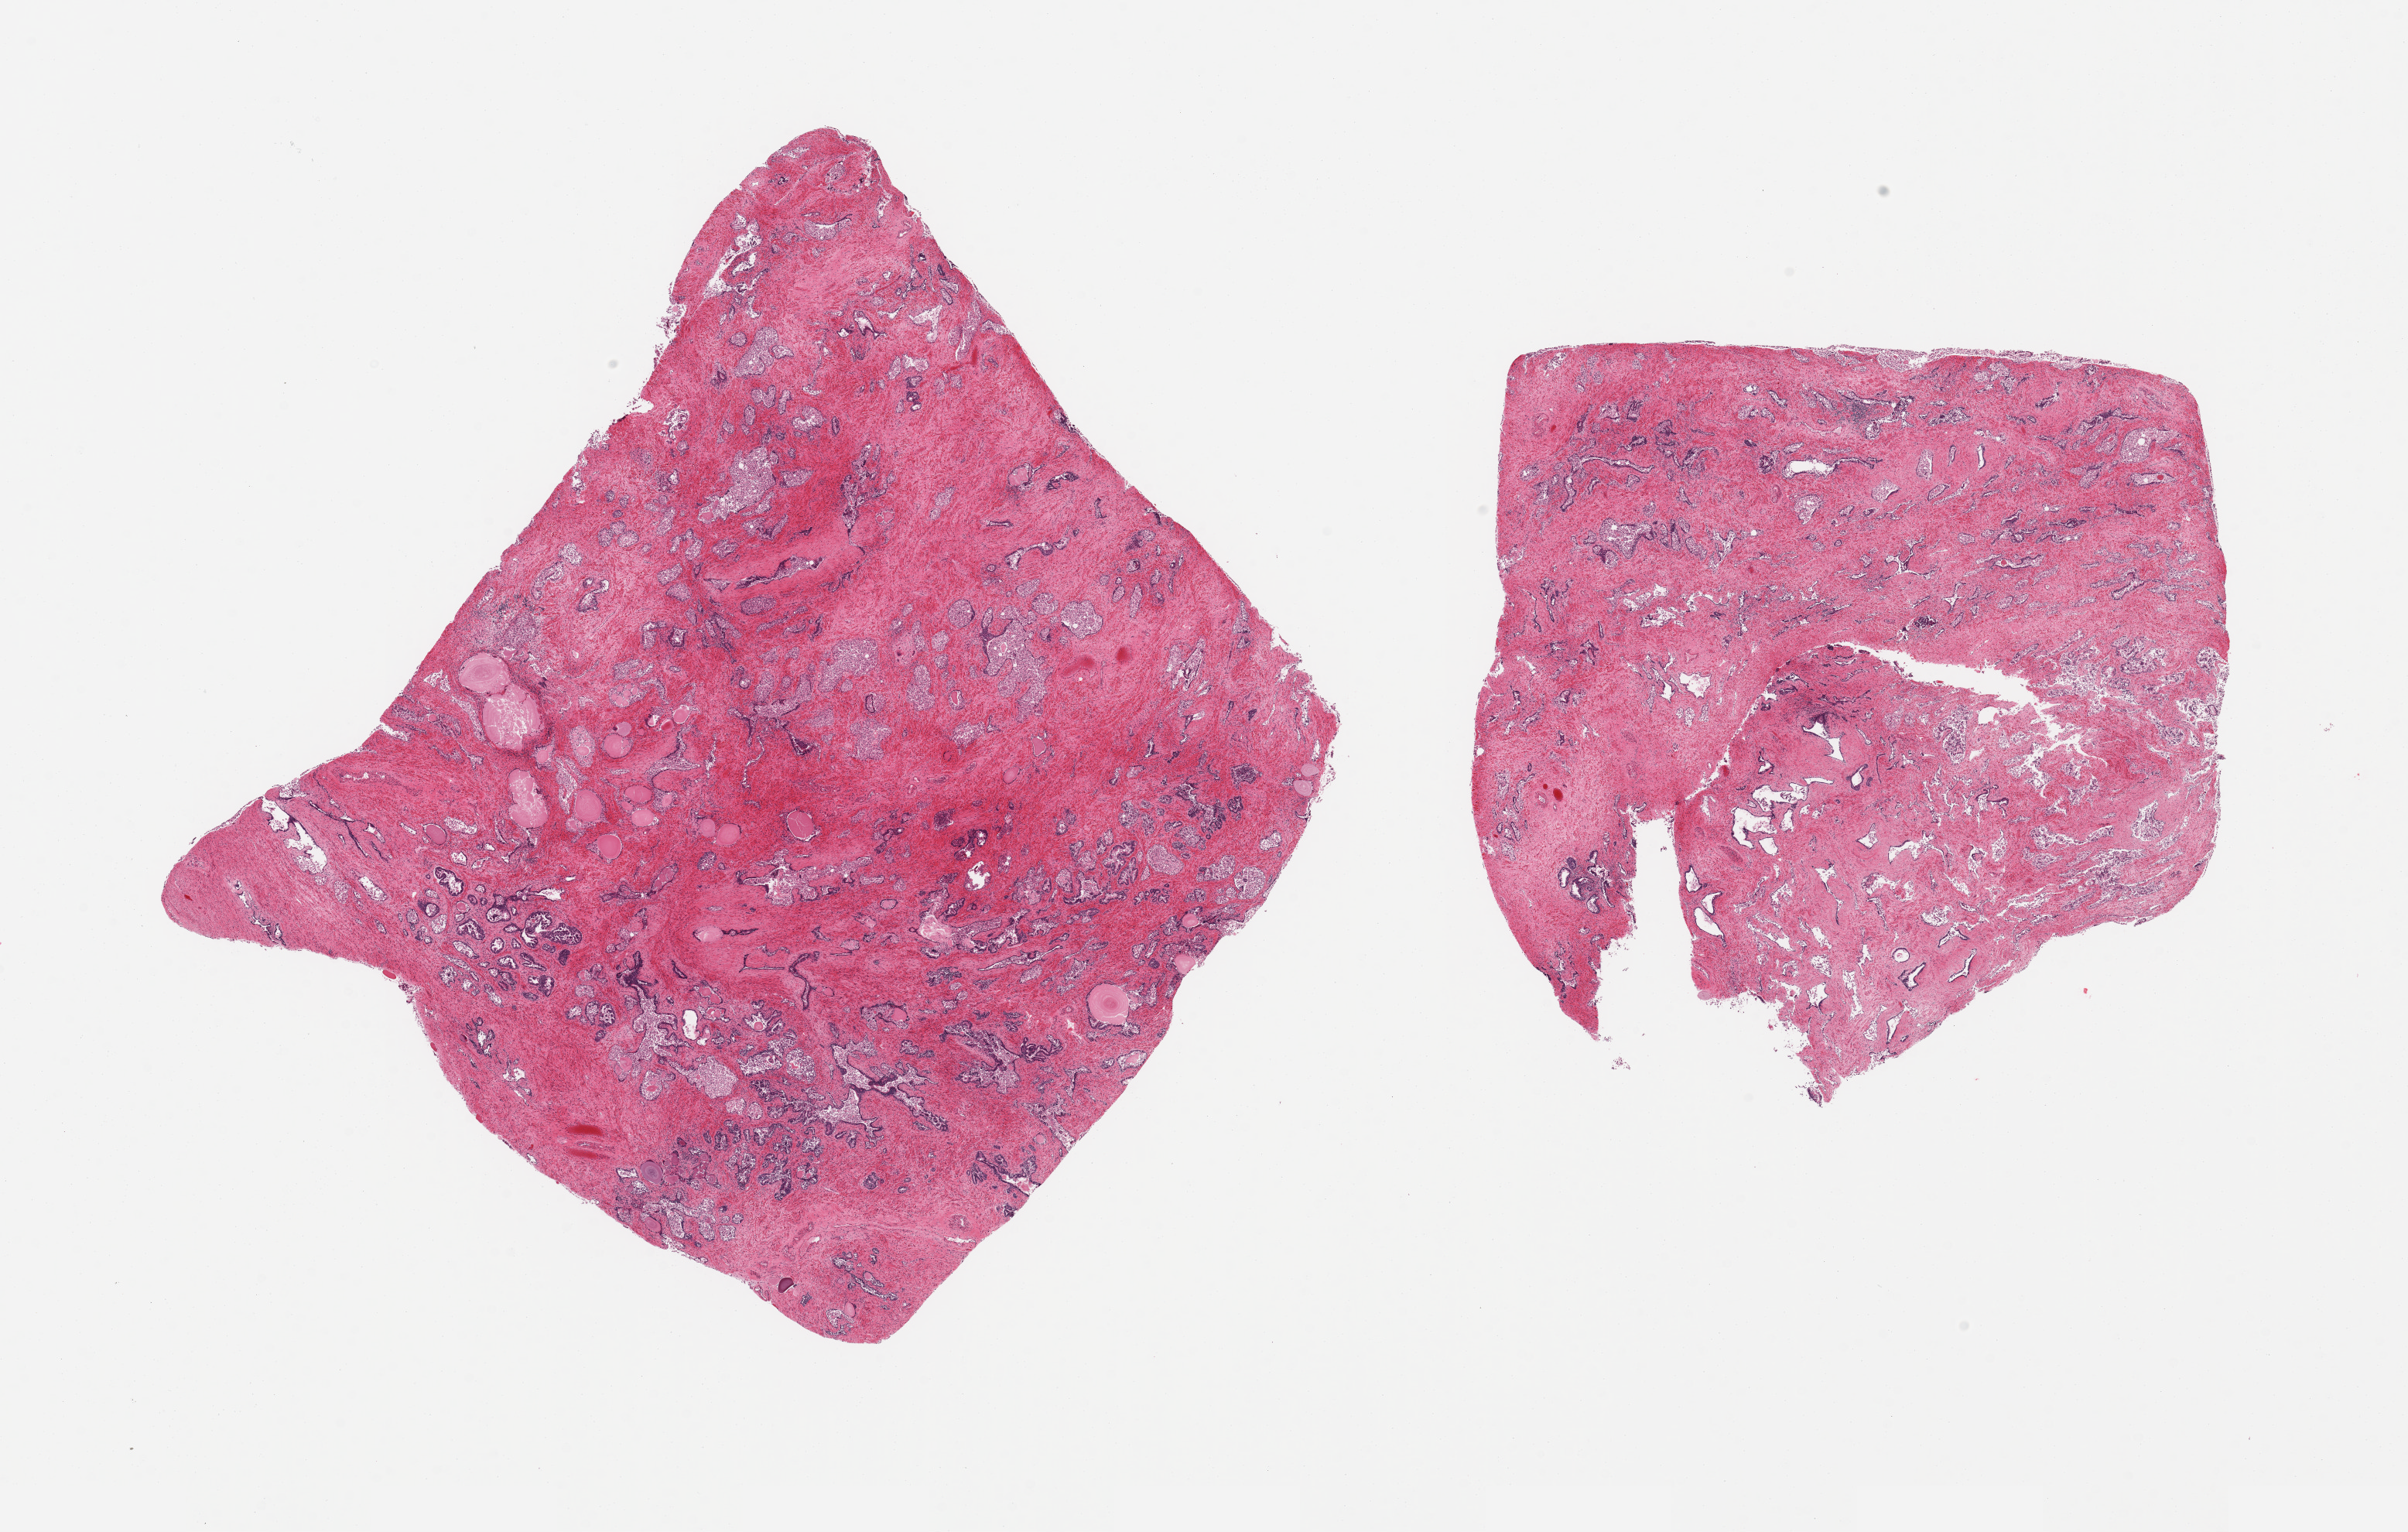
Whole-slide image, haematoxylin and eosin stain, brightfield — low-resolution overview of the scanned area, about 24.6 x 15.7 mm (acquisition: 20x scan), PAXgene-fixed, paraffin-embedded tissue, sampled site (target tissue): prostate, donor tissue sample.
Reviewer comment on this tissue sample: 2 pieces; glandular hyperplasia and prostatitis; severe autolysis of epithelium, stroma intact.